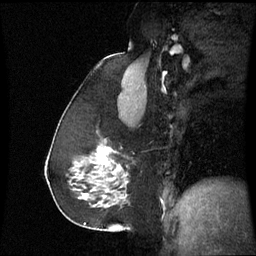
Breast MRI (dynamic contrast-enhanced), one sagittal slice. Position 37 of 60 along the scan axis. Dynamic contrast-enhanced series, image 2 of 3 at this slice position (ordered by acquisition). 1.5 T. TE 4.2 ms, TR 8.9 ms. 2.4 mm slice thickness. 256 × 256 image matrix, field of view 220 × 220 mm. Patient: female, 59 years. Case-level facts recorded for this patient, not image findings: setting: breast cancer imaged before/during neoadjuvant chemotherapy; receptor status: triple-negative.
Structures marked on this image (semi-automatic segmentation, software-assisted and operator-edited):
- analysis volume of interest (the breast-tissue region the enhancement analysis was run in; not a lesion): box from (x=88, y=140) to (x=129, y=197) px
- tumour enhancement mask (voxels above the 70 % enhancement threshold inside the analysis volume of interest): (x=100, y=148)–(x=121, y=173)